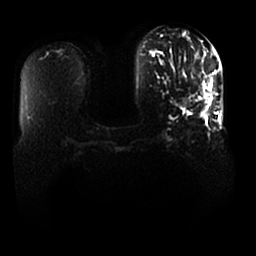
Breast MRI, one axial slice; position 5 of 25 along the scan axis; diffusion-weighted series; image 2 of 4 stored at this slice position (different b-values; order by instance number); 1.5 T; 256 × 256 image matrix, field of view 370 × 370 mm. Female patient.
Annotated regions visible in this slice (manually delineated by an expert):
- tumour on diffusion-weighted imaging: bounding box <182,75,212,106> (left, top, right, bottom; pixels)